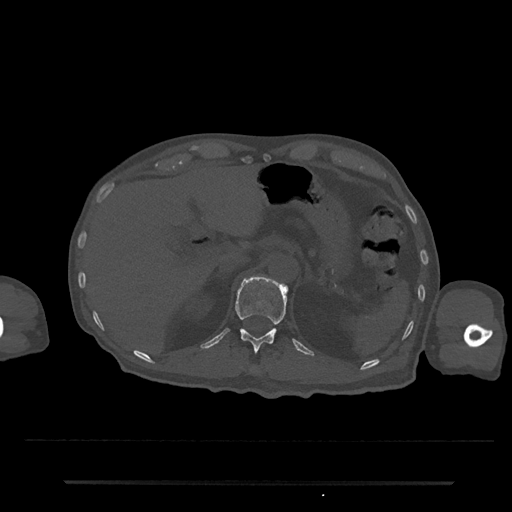
CT including the spine, one axial slice. Position 191 of 797 along the scan axis. Reconstruction kernel Br40s/3. 120 kVp. Bone window (W 1800 / L 400 HU). 0.5 mm slice thickness. 512 × 512 image matrix, field of view 427 × 427 mm. Patient: male, 74 years. From the clinical record (not read from this slice): primary cancer: prostate.
Annotated regions visible in this slice (semi-automatic segmentation, software-assisted and operator-edited):
- T11 vertebra: bounding box <253,368,256,370> (left, top, right, bottom; pixels)
- T12 vertebra: <235,277,287,352>